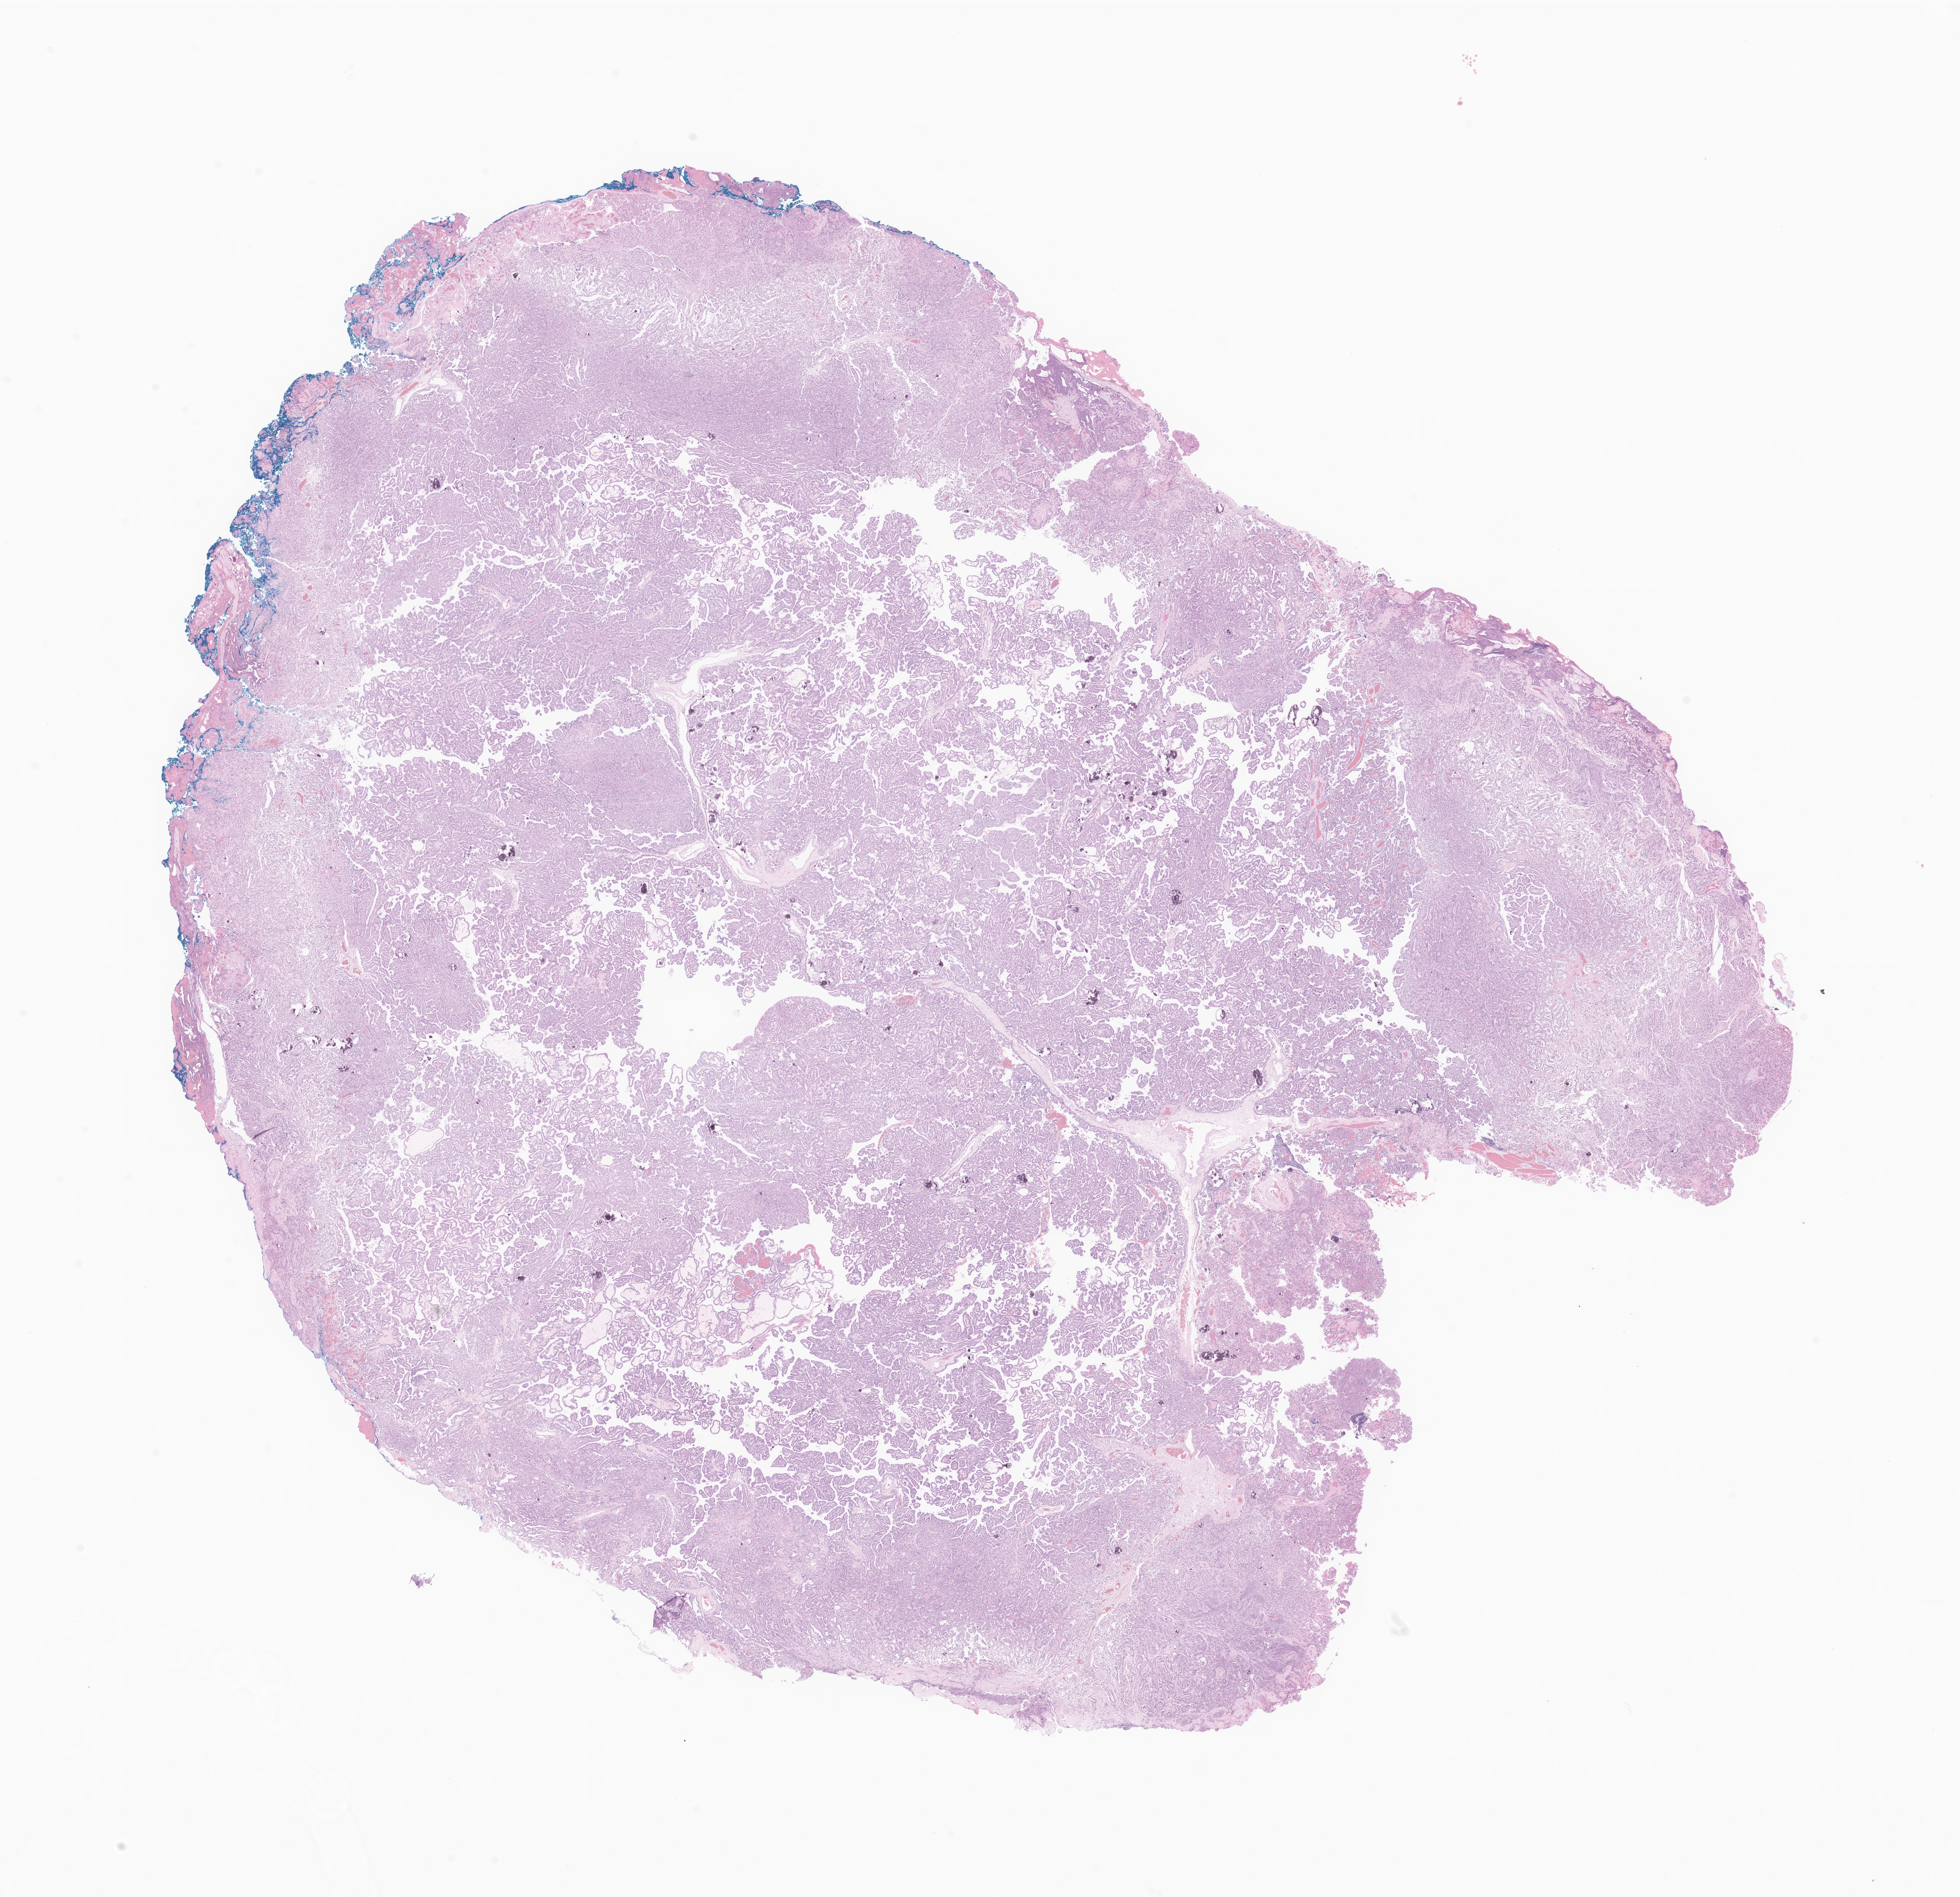
Haematoxylin and eosin whole-slide image of tumor tissue from the brain — a low-resolution overview of the entire scanned area, about 22.3 x 21.6 mm, FFPE section. Female patient, age 210 months (17 years 6 months).
- recorded diagnosis: Choroid plexus papilloma, NOS